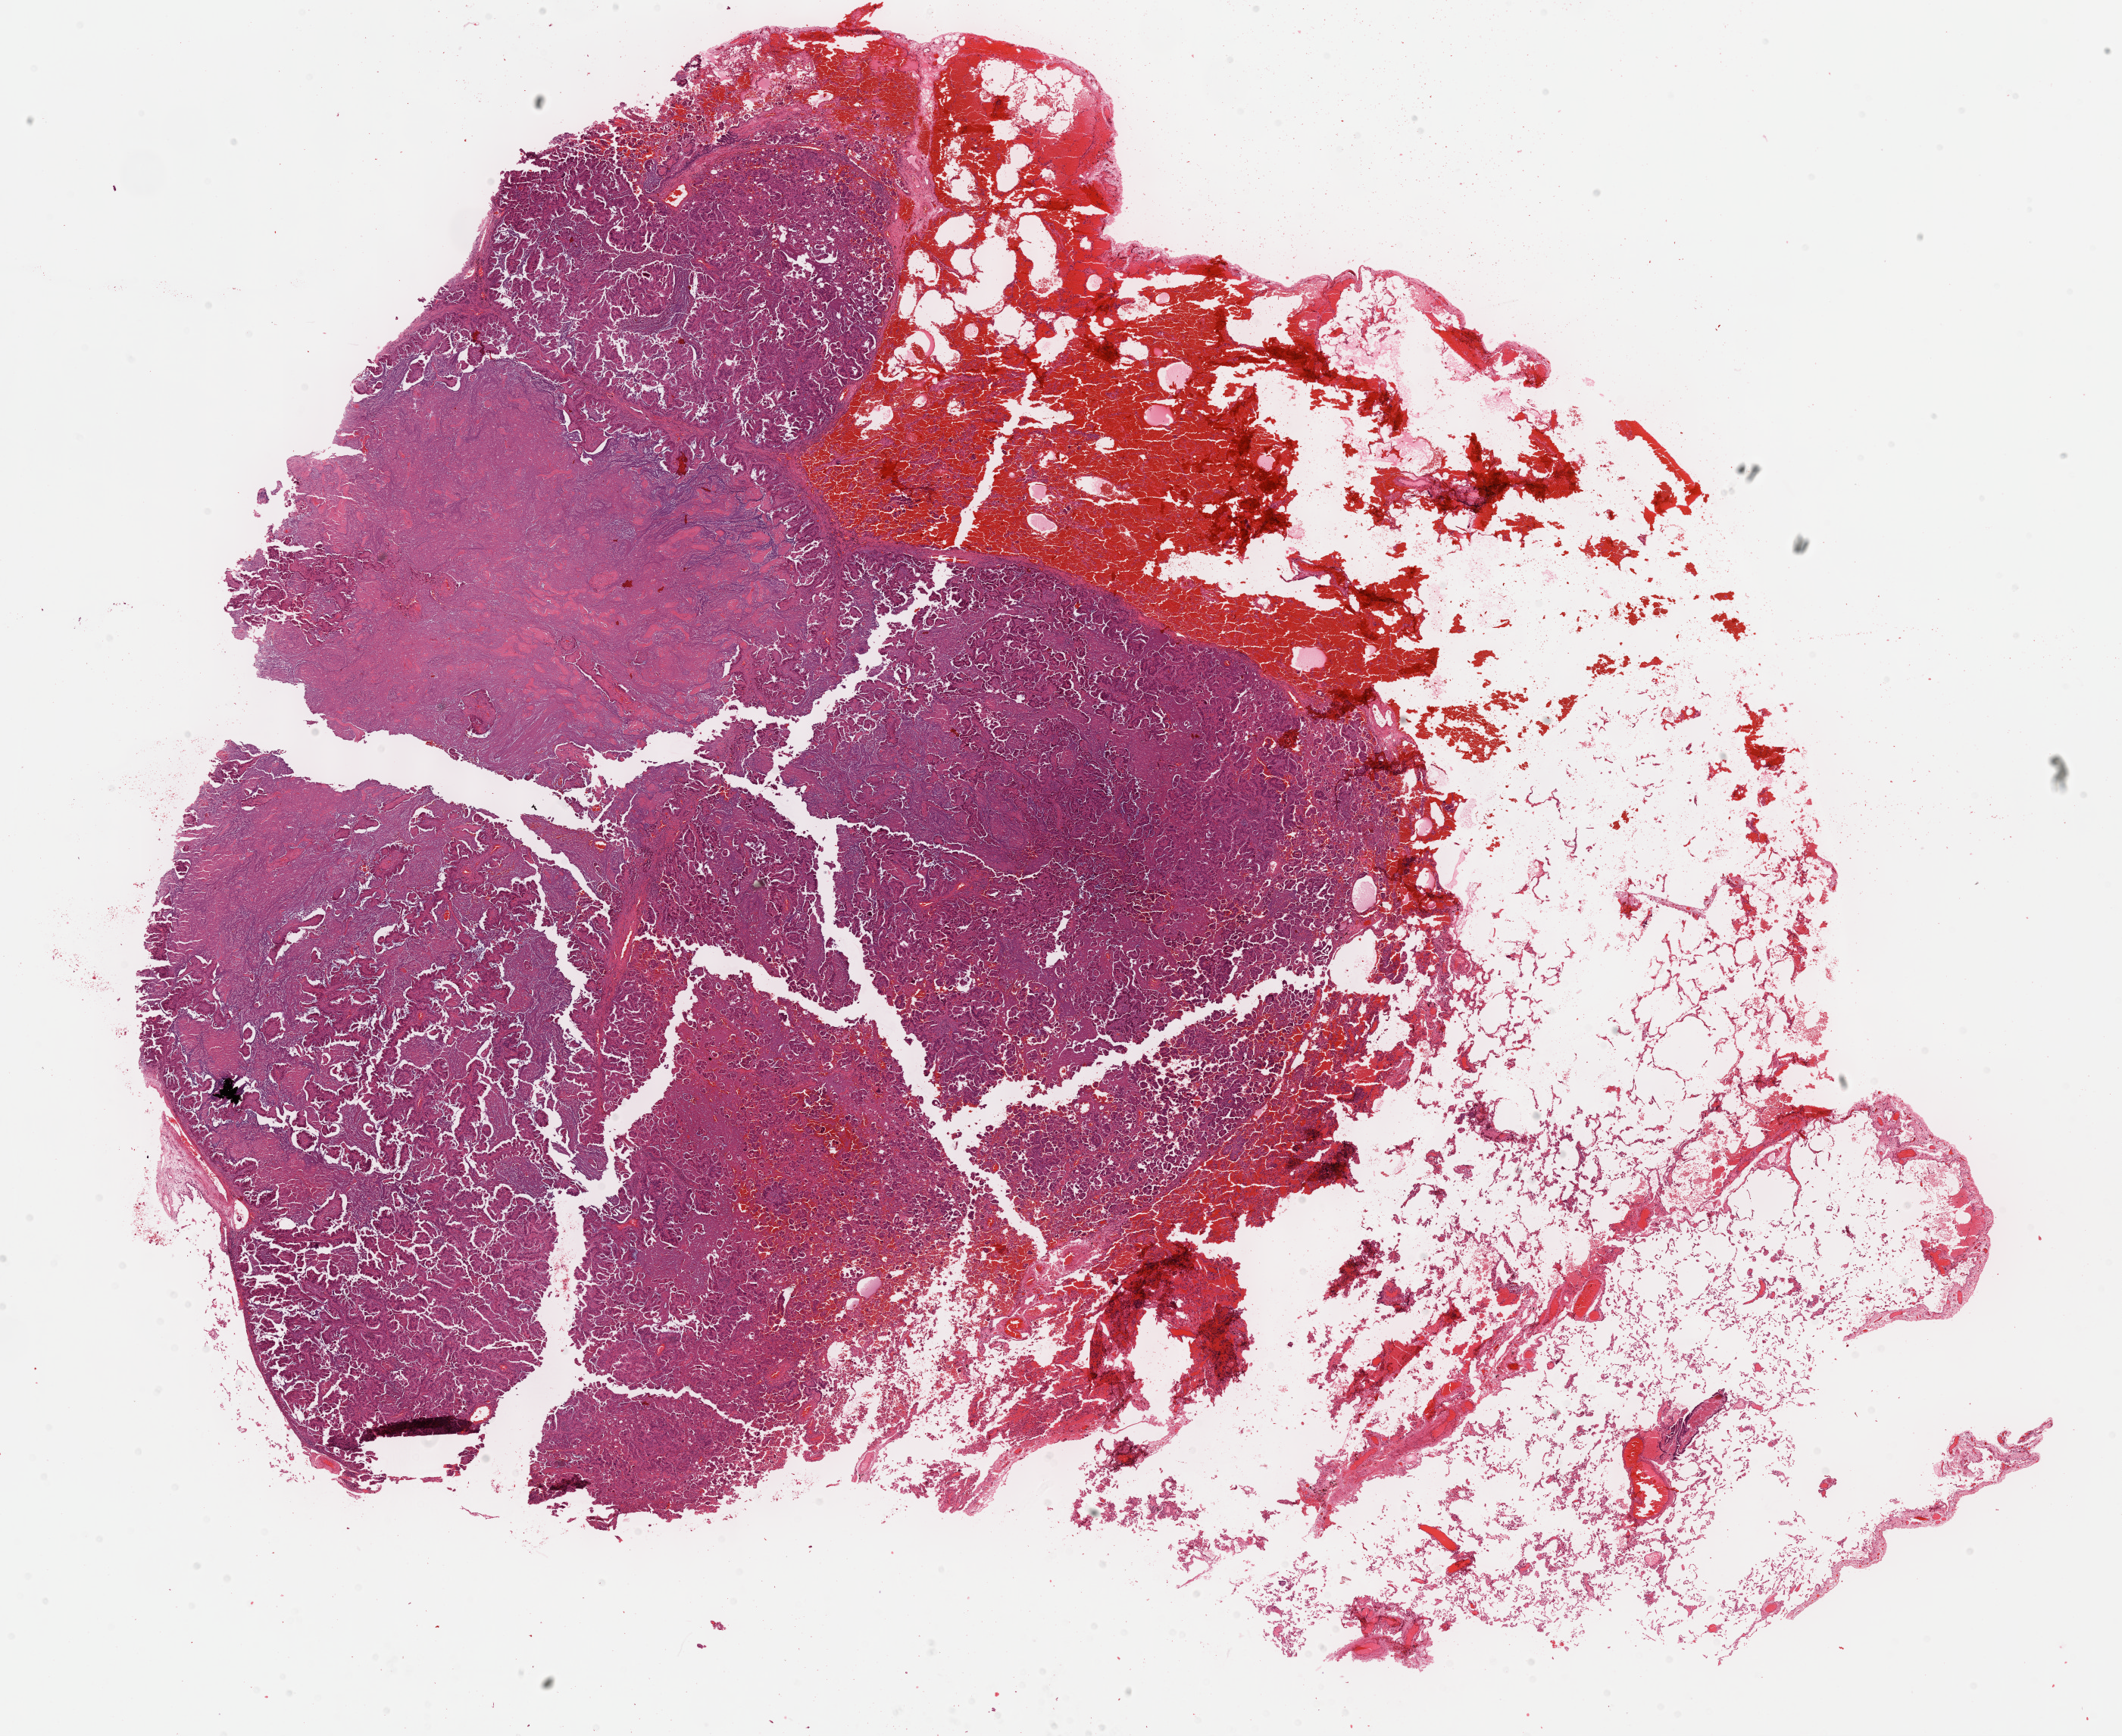
Whole-slide histology image, H&E, low-resolution overview of the scanned area, about 22.7 x 18.5 mm (slide scanned at 40x). Formalin-fixed paraffin-embedded (FFPE) diagnostic section. Sample: primary tumour, lung. Patient: male, age at initial diagnosis 64 years.
Diagnosis: Papillary adenocarcinoma, NOS (lower lobe, lung).